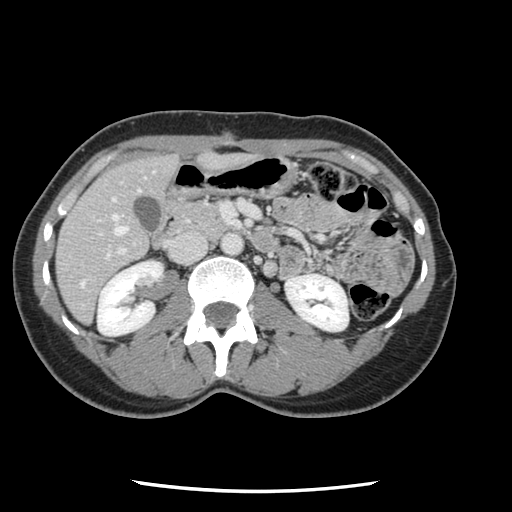
Contrast-enhanced abdominal CT, one axial slice; position 43 of 134 along the scan axis; 120 kVp; intravenous contrast given; soft-tissue window (W 400 / L 40 HU); 512 × 512 image matrix, field of view 330 × 330 mm. Female patient, age 43 years. Case-level facts recorded for this patient, not image findings: diagnosis: colorectal cancer liver metastases, imaged before liver resection; multiple liver metastases: yes; largest metastasis: 3.4 cm; disease in both lobes: yes.
Structures marked on this image (expert manual segmentation):
- hepatic veins: bounding box [x1, y1, x2, y2] px = [80, 190, 140, 287]
- liver: [58, 155, 178, 321]
- planned liver remnant (the part of the liver to remain after resection): [57, 155, 178, 322]
- portal vein (with intrahepatic branches): [98, 201, 259, 261]